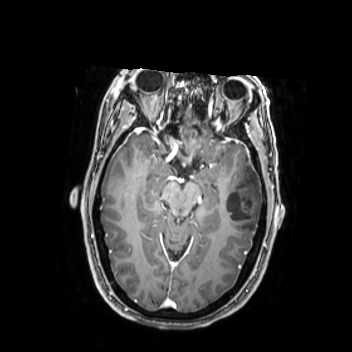
Brain MRI from a brain-tumour surgery series, one axial slice; slice 158 of 350 in the series (ordered by position); T1-weighted post-contrast; 0.9 mm slice thickness; 352 × 352 image matrix, field of view 280 × 280 mm. From the clinical record (not read from this slice): histopathology: Oligodendroglioma; WHO grade: 2; IDH mutation: yes; tumour location: Left Middle Temporal Gyrus.
Outlined on this slice (outlined manually by an expert reader):
- tumour: bounding box <224,163,262,236> (left, top, right, bottom; pixels)